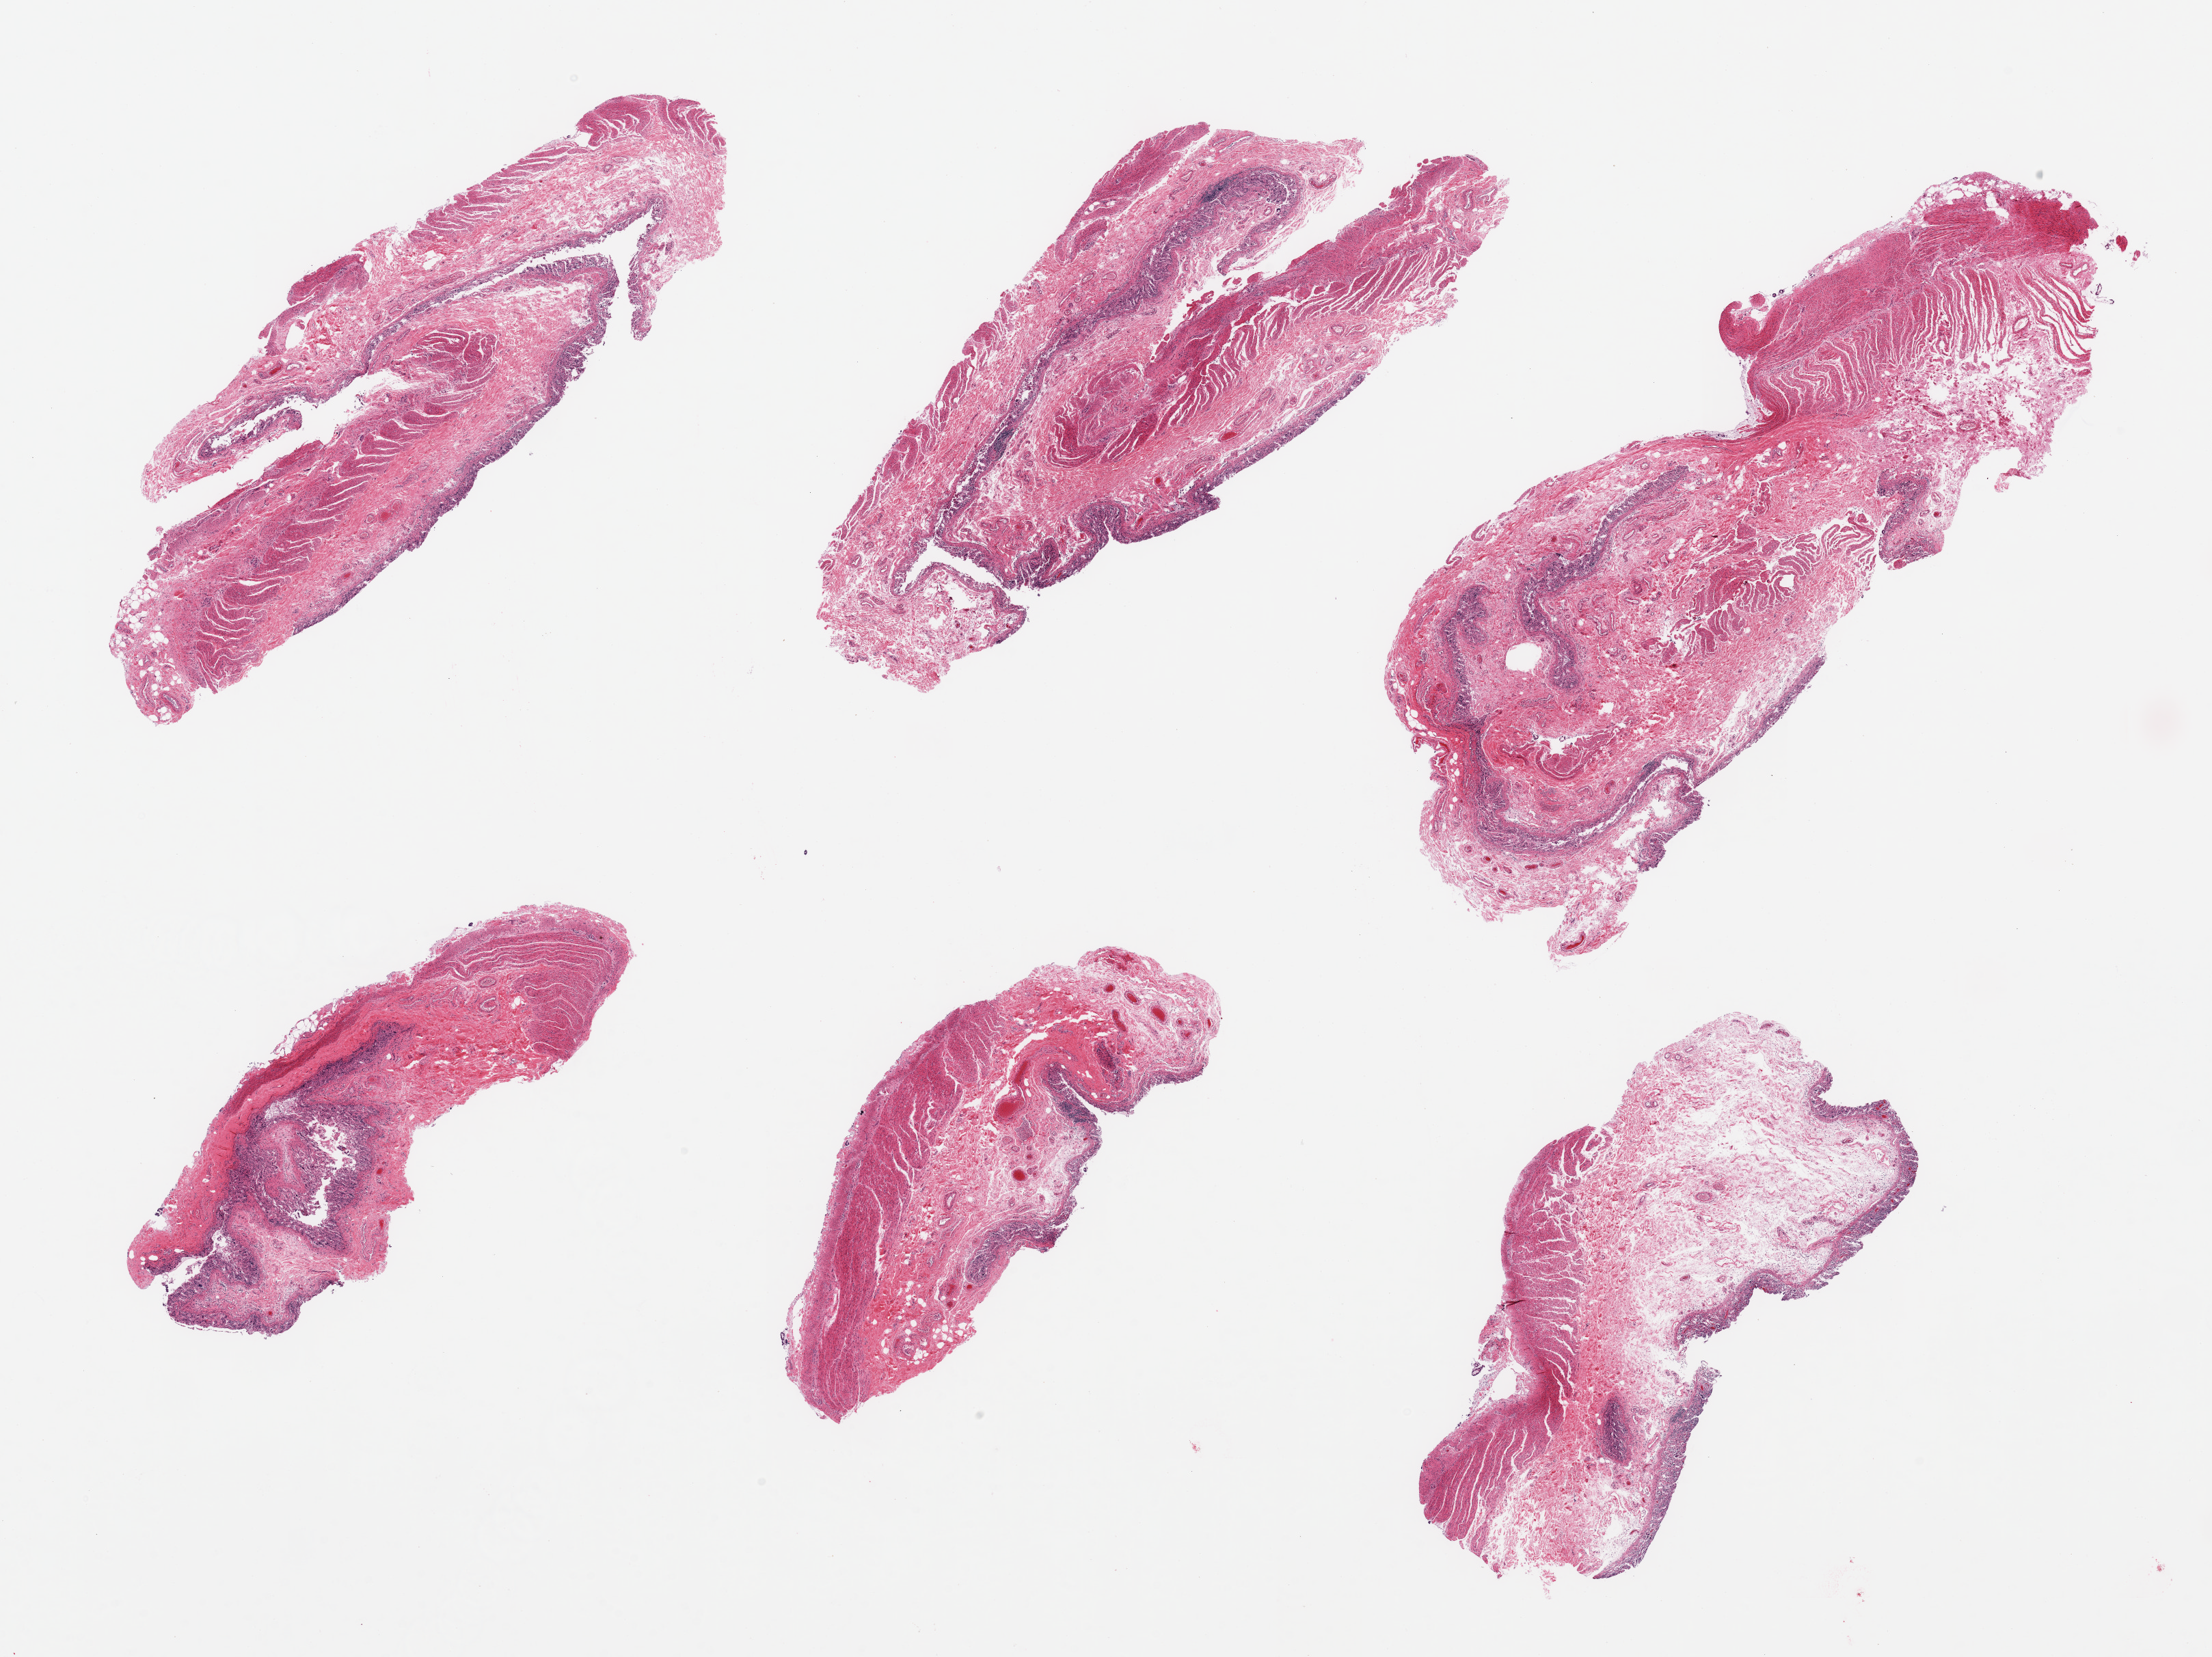
Digitized H&E-stained section — whole scanned area (about 25.6 x 19.2 mm, from a 20x scan) shown as a low-resolution overview. PAXgene-fixed paraffin-embedded (PFPE) section. Sampled site (target tissue): transverse colon. Donor tissue sample. Male donor.
Review note (as recorded): 6 pieces; target mucosa up to ~0.2mm; glandular elements sloughed, lamina propria remains.